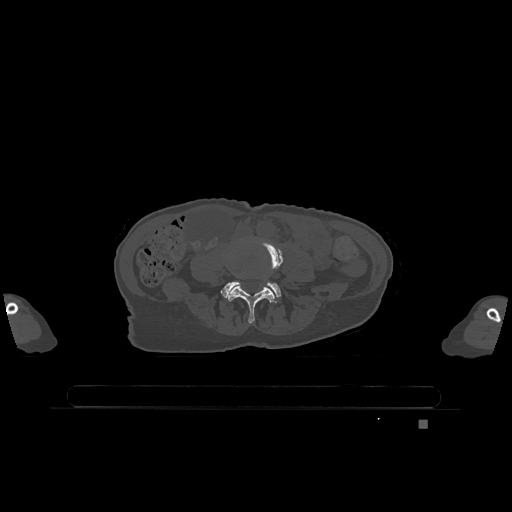
CT including the spine, one axial slice. Slice 278 of 1317 in the series (ordered by position). Bone window (W 1800 / L 400 HU). 0.5 mm slice thickness. 512 × 512 image matrix, field of view 500 × 500 mm. Patient: female, 74 years. From the clinical record (not read from this slice): primary cancer: lung.
Structures marked on this image (semi-automatic segmentation, software-assisted and operator-edited):
- L4 vertebra: bounding box [x1, y1, x2, y2] px = [227, 241, 283, 323]
- L5 vertebra: [221, 281, 281, 301]